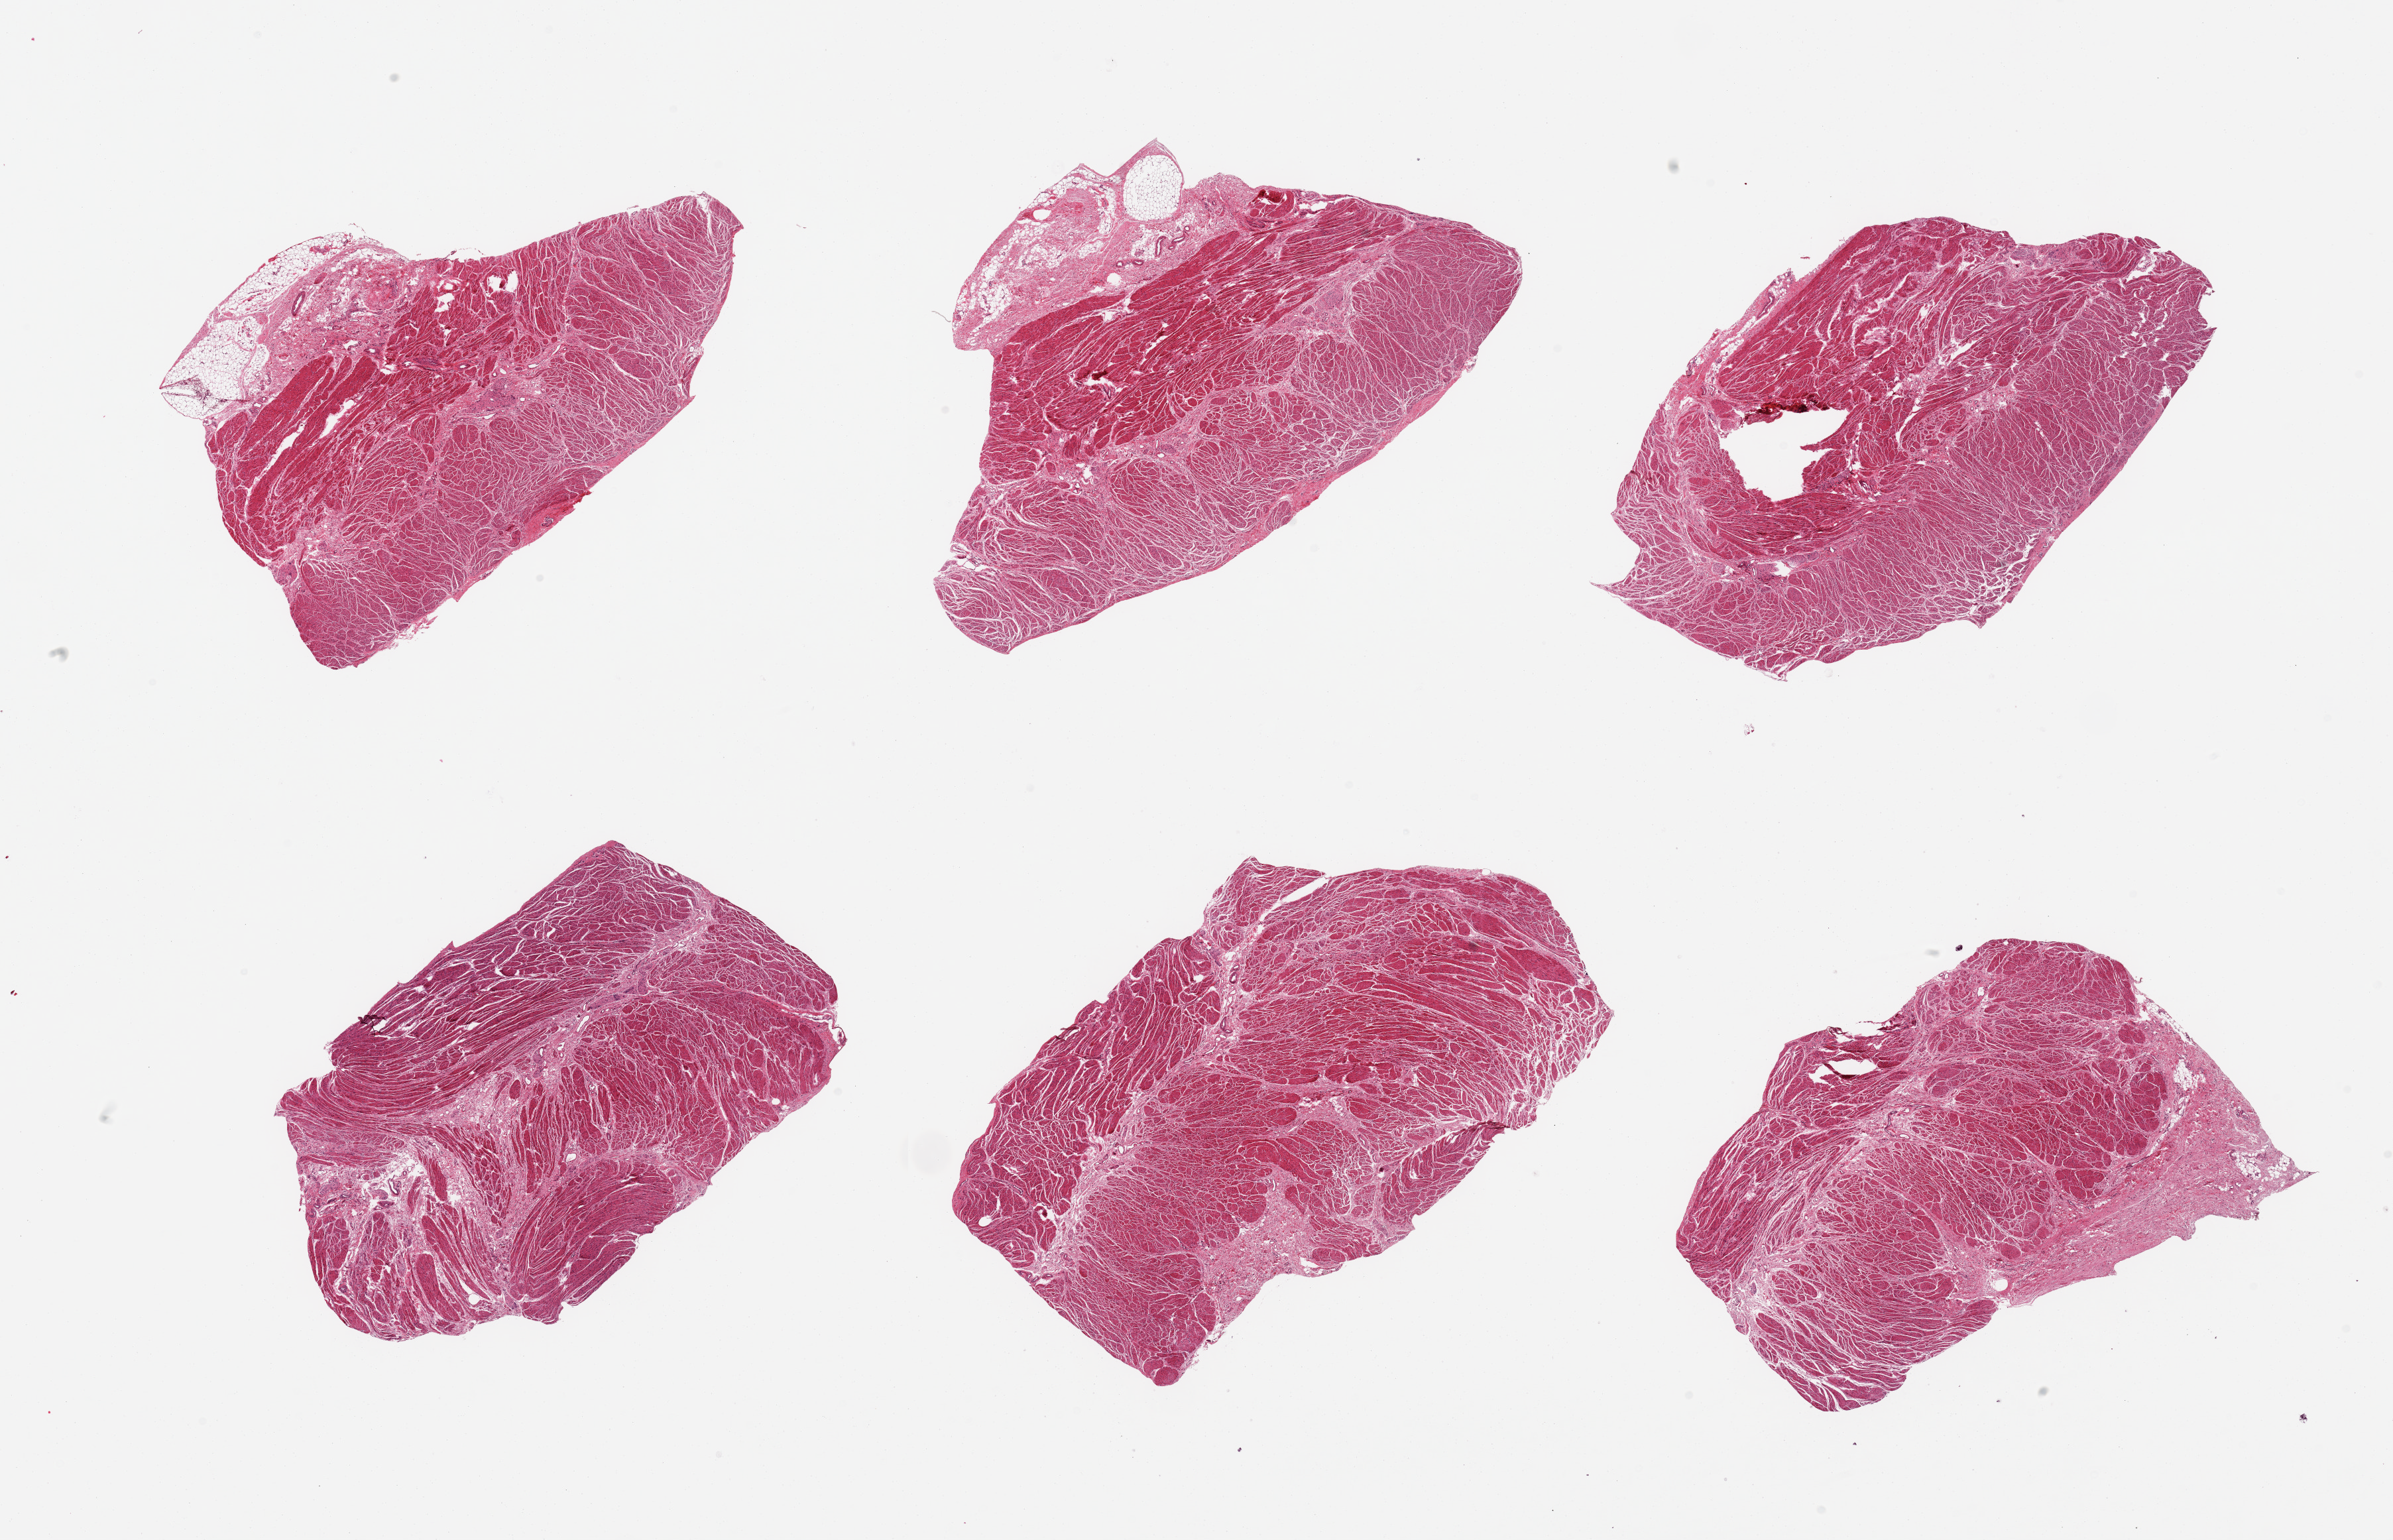
Whole-slide image, hematoxylin and eosin (H&E) stain, low-resolution overview of the scanned area, about 28.5 x 18.4 mm. PAXgene-fixed paraffin-embedded (PFPE) section. Target tissue: gastroesophageal junction. Donor tissue sample. Donor sex: male.
- review note (as recorded): 6 pieces; 10% & 20% fibrofatty stroma on 2 pieces